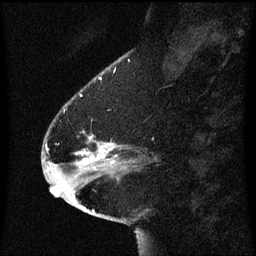
Breast MRI (dynamic contrast-enhanced), one sagittal slice. Position 18 of 60 along the scan axis. Dynamic contrast-enhanced series, image 2 of 3 at this slice position (ordered by acquisition). 1.5 T. TE 4.2 ms, TR 8.4 ms. 256 × 256 image matrix, field of view 200 × 200 mm. Female patient, age 54 years. From the clinical record (not read from this slice): setting: breast cancer imaged before/during neoadjuvant chemotherapy; receptor status: HR-positive, HER2-negative.
Annotated regions visible in this slice (semi-automatically segmented with operator editing):
- analysis volume of interest (the breast-tissue region the enhancement analysis was run in; not a lesion): bounding box (x1, y1, x2, y2) in pixels: (46, 104, 123, 171)
- tumour enhancement mask (voxels above the 70 % enhancement threshold inside the analysis volume of interest): (87, 146, 111, 159)